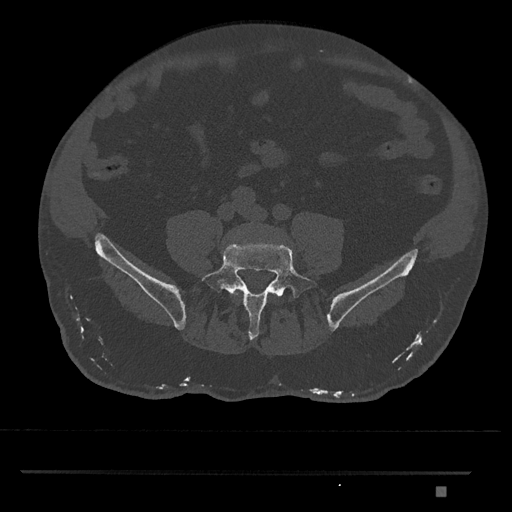
CT including the spine, one axial slice; position 564 of 1134 along the scan axis; reconstruction kernel Br40s/3; 120 kVp; bone window (W 1800 / L 400 HU); 0.5 mm slice thickness; 512 × 512 image matrix. Patient: male, 65 years. Case-level facts recorded for this patient, not image findings: primary cancer: prostate.
Structures marked on this image (semi-automatically segmented with operator editing):
- L4 vertebra: box from (x=231, y=291) to (x=277, y=299) px
- L5 vertebra: (x=201, y=243)–(x=318, y=340)